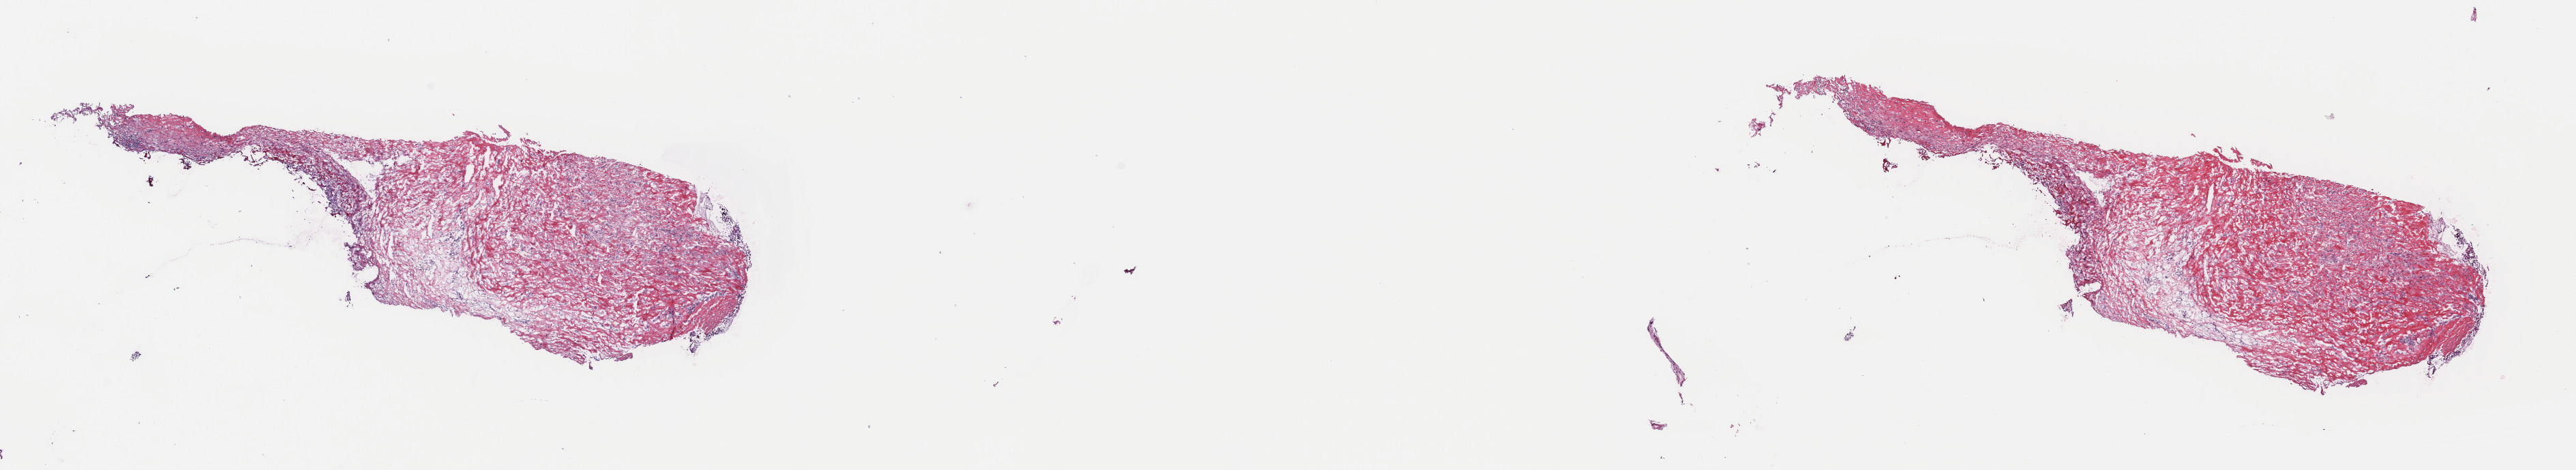
Hematoxylin and eosin (H&E) stained whole-slide image, low-resolution overview of the scanned area, about 29.8 x 5.4 mm (slide scanned at 40x). Frozen section from the top of the tissue portion. Sample: primary tumour, mesothelium. Female patient; age at initial diagnosis 64 years. Pathologist review of this section (percent, as recorded): tumour cells 100%, tumour nuclei 75%, normal cells 0%, stromal cells 0%, necrosis 0%. Infiltration values recorded for this section: lymphocyte infiltration 2%, monocyte infiltration 0%, neutrophil infiltration 0%.
AJCC pathologic stage: IV (7th edition). Laterality: left. Pathologic diagnosis: Epithelioid mesothelioma, malignant.